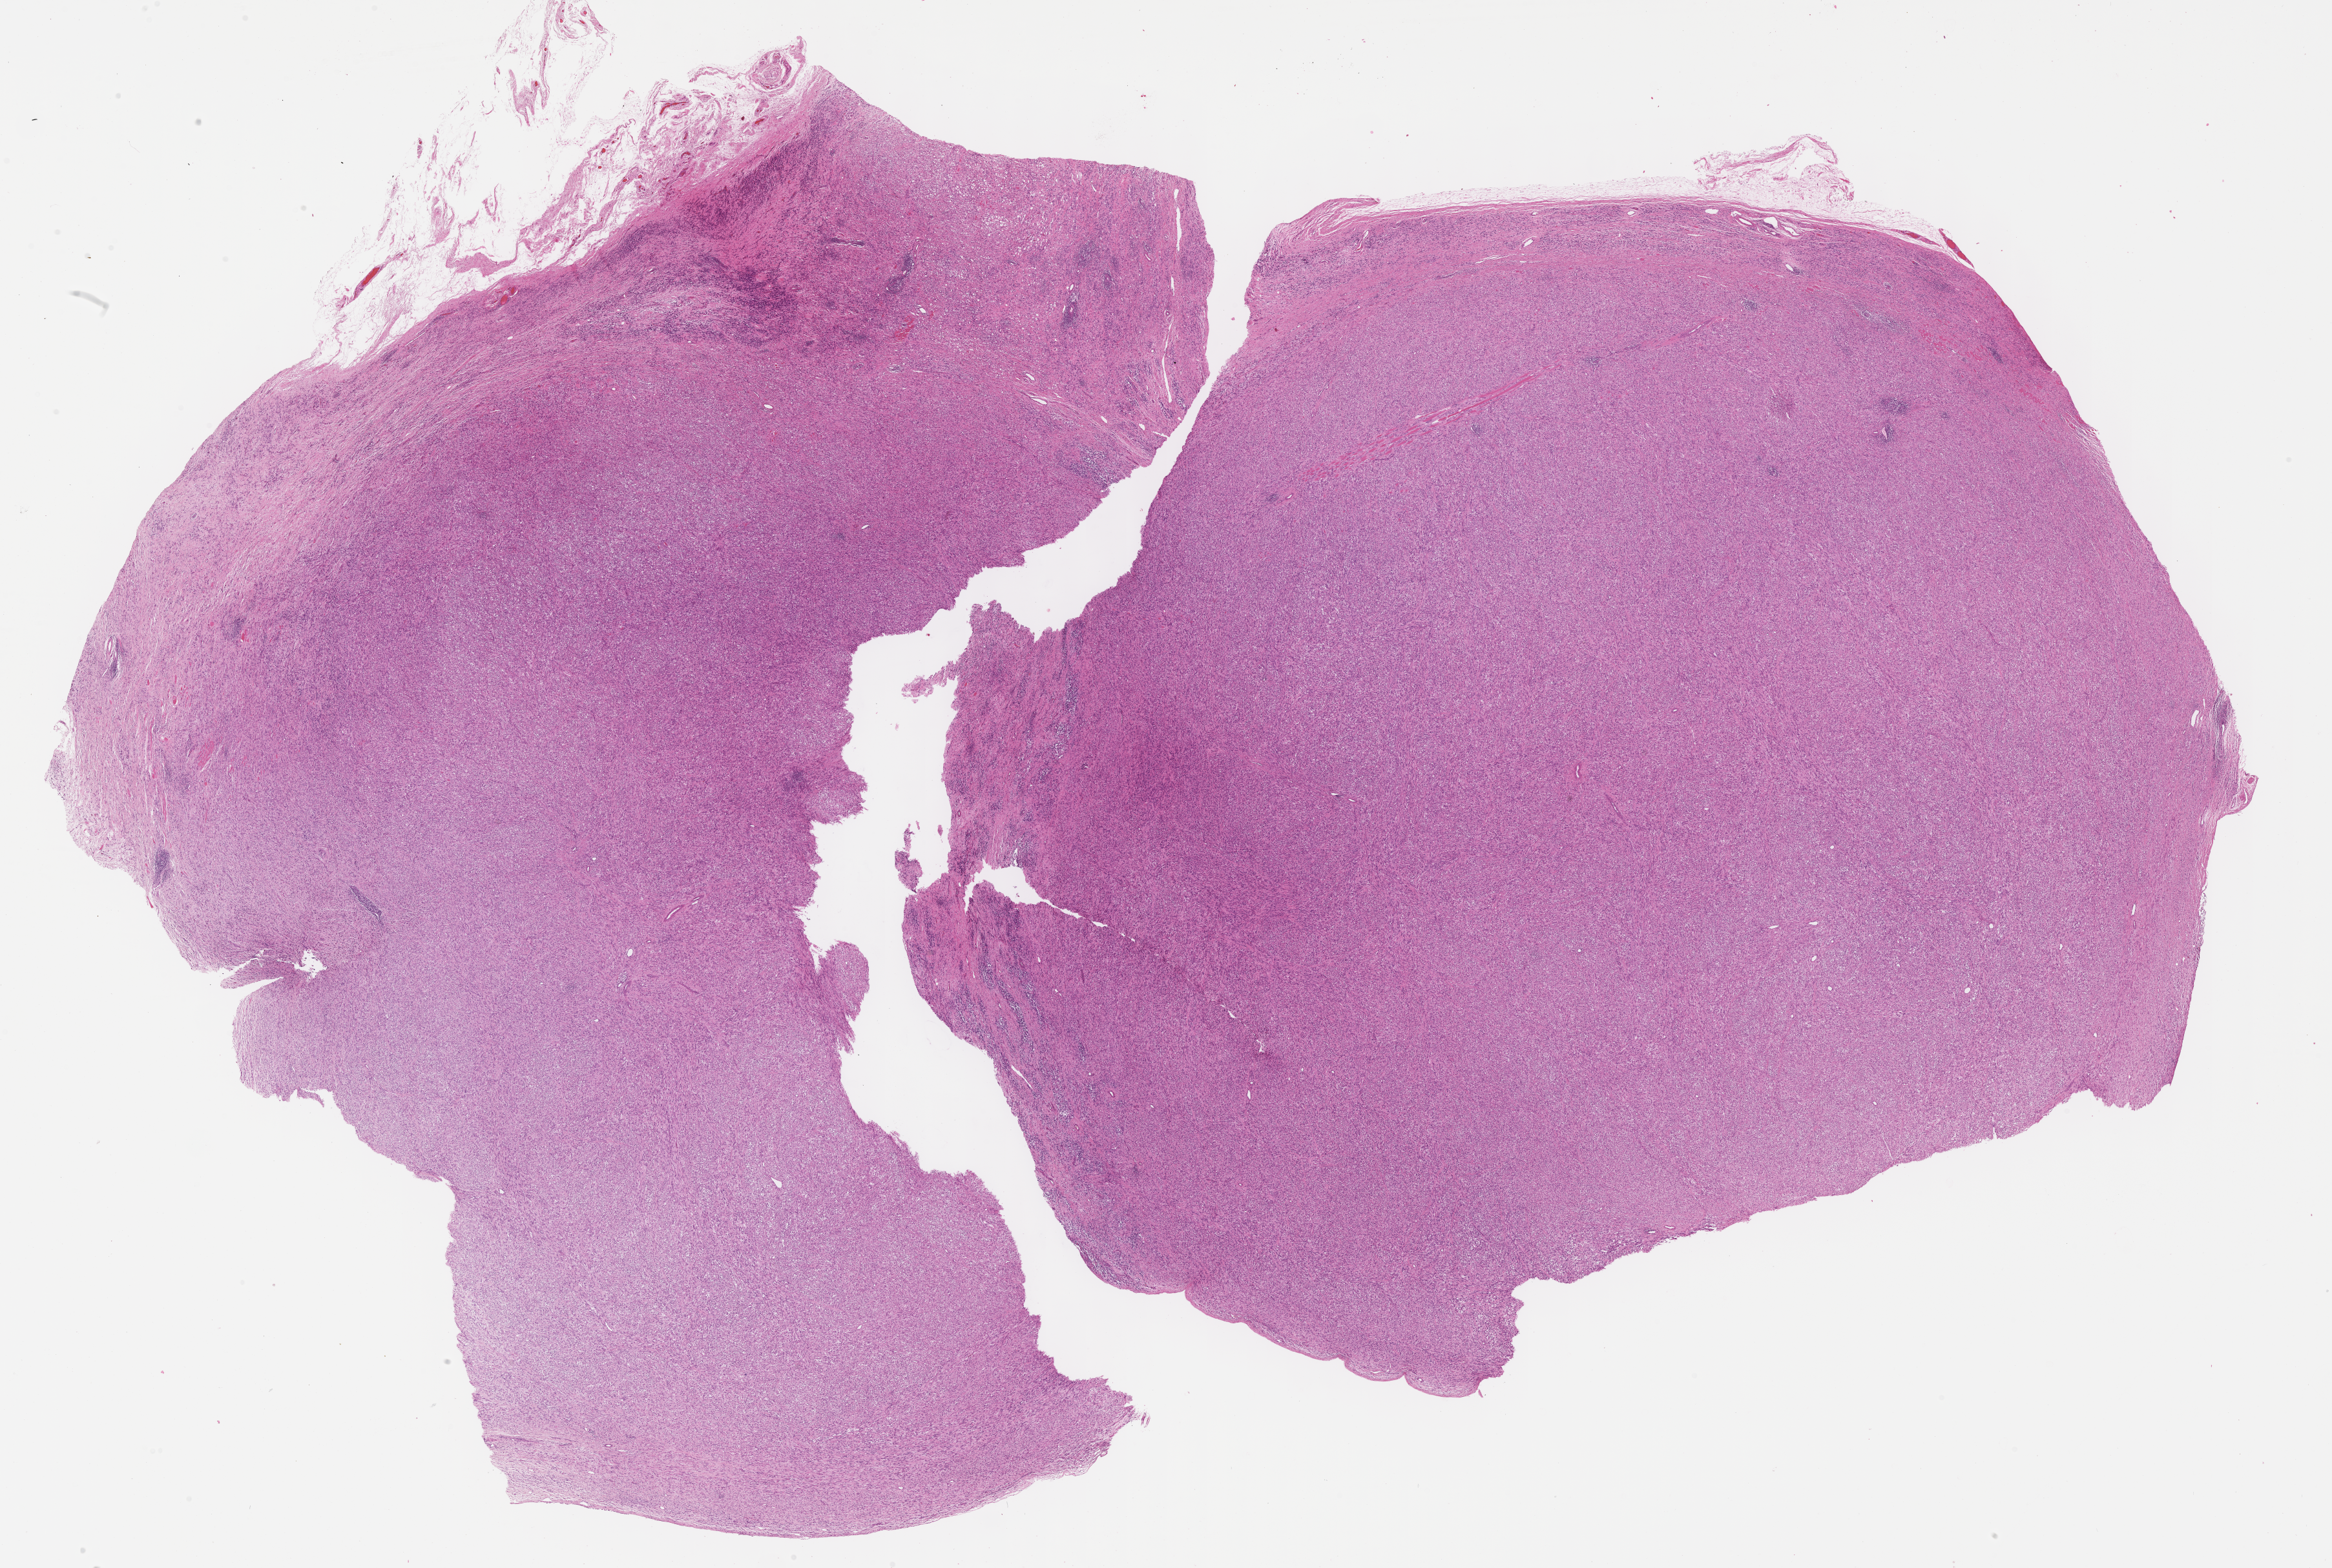
Hematoxylin and eosin (H&E) whole-slide image of tumor tissue — low-resolution overview of the scanned area, about 29.2 x 19.6 mm; formalin-fixed, paraffin-embedded (FFPE) tissue; sample anatomic site: testis, left. Patient: male, age 4.0 years at diagnosis.
Primary site (case record): testis-paratesticular. Metastatic status at presentation (as recorded): non-metastatic (confirmed). Stage (as recorded): 1. Diagnosis: rhabdomyosarcoma; histological classification: embryonal rhabdomyosarcoma.